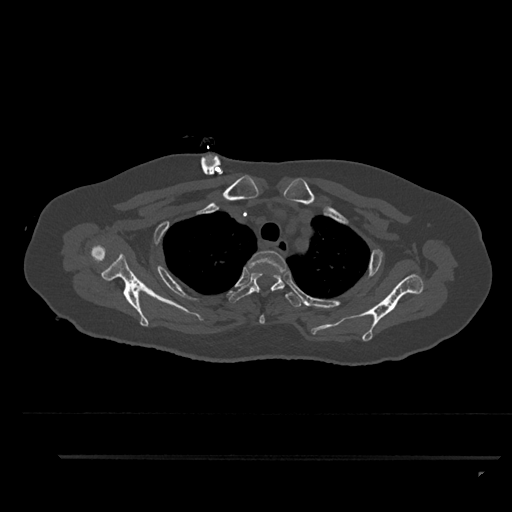
CT including the spine, one axial slice. 120 kVp. Bone window (W 1800 / L 400 HU). 0.5 mm slice thickness. 512 × 512 image matrix, field of view 408 × 408 mm. Female patient, age 44 years. Case-level facts recorded for this patient, not image findings: primary cancer: renal.
Structures marked on this image (semi-automatically segmented with operator editing):
- T2 vertebra: bounding box (x1, y1, x2, y2) in pixels: (248, 251, 287, 324)
- T3 vertebra: (228, 271, 304, 307)